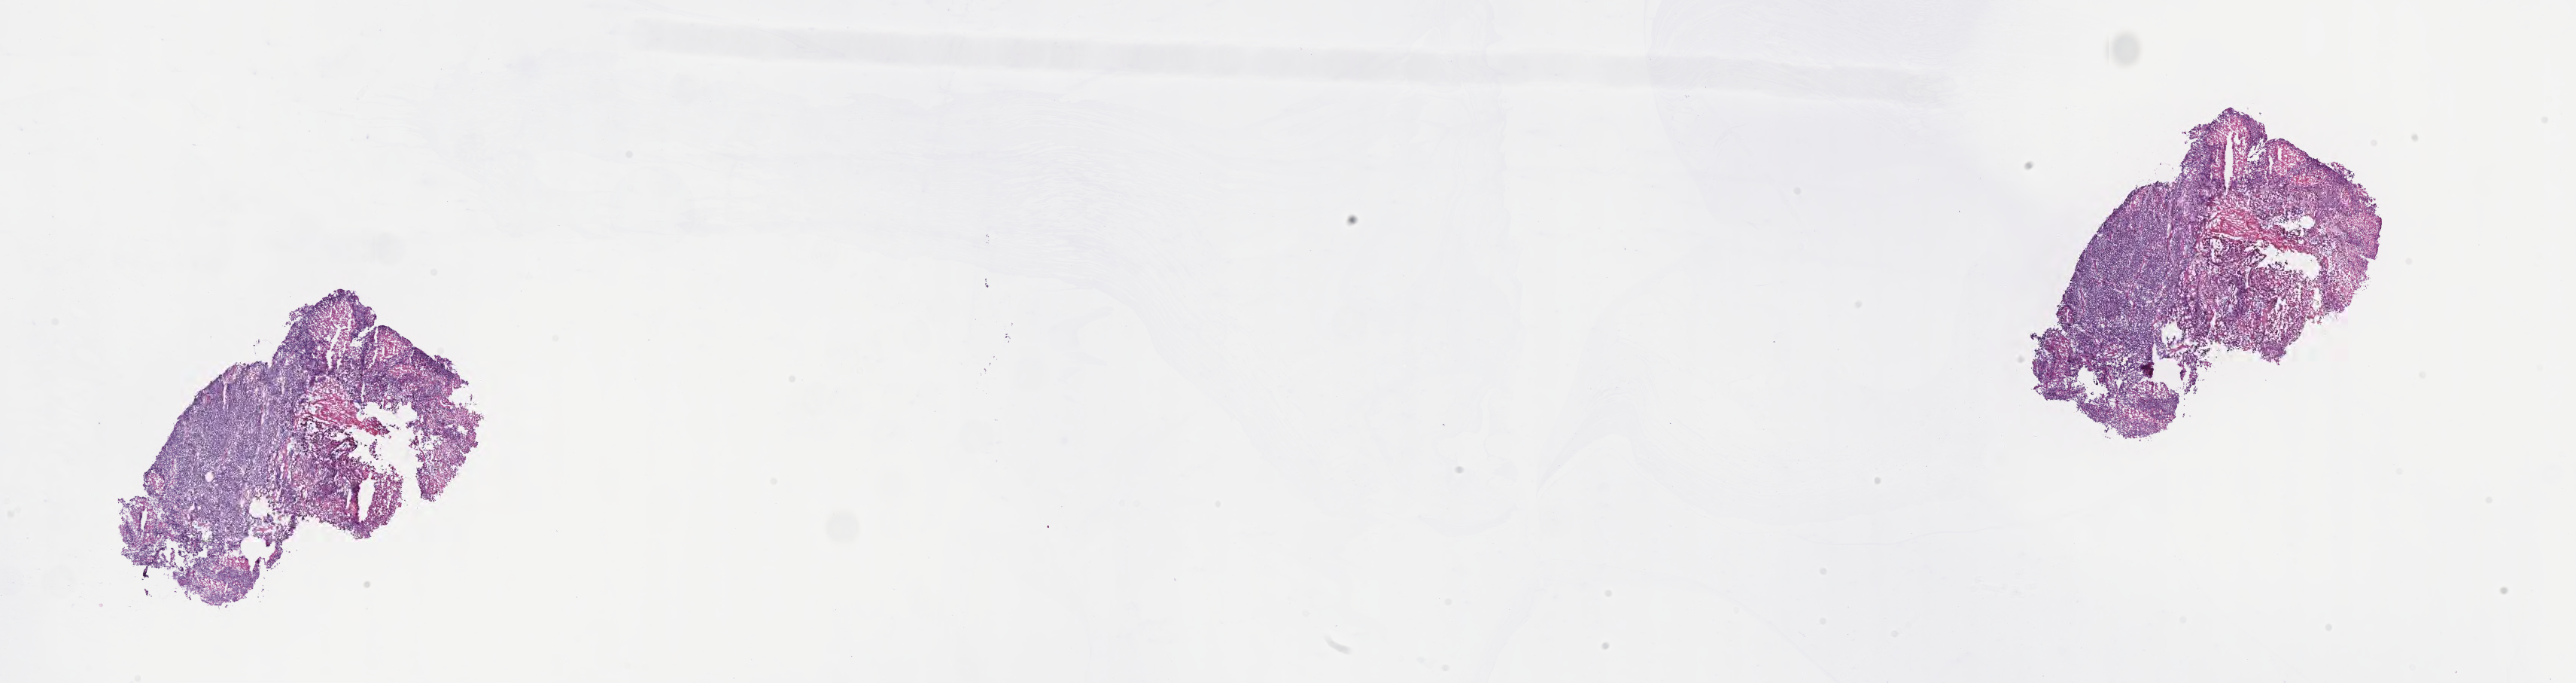
Whole-slide image, haematoxylin and eosin stain of tumor tissue from the kidney — whole scanned area (about 27.7 x 7.3 mm) shown as a low-resolution overview, frozen section (OCT-embedded). Male patient, age 191 months (15 years 11 months).
Diagnosis: Ewing sarcoma.